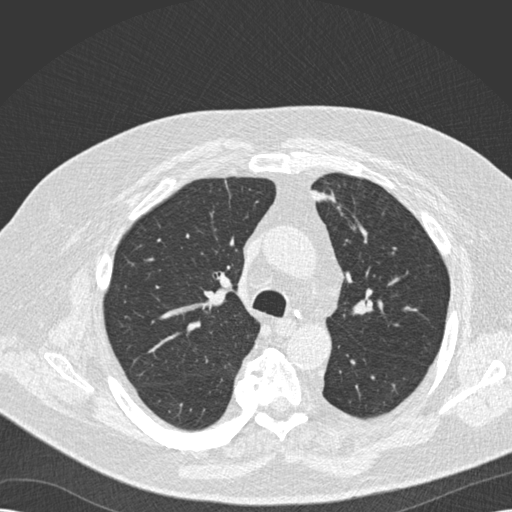
Low-dose screening chest CT, one axial slice. Slice 115 of 173 in the series (ordered by position). Reconstruction kernel B30f. 120 kVp. Lung window (W 1500 / L -600 HU). 512 × 512 image matrix, field of view 370 × 370 mm.
Annotated regions visible in this slice (manually delineated by an expert):
- lesion 1 (tumor, upper lobe of left lung): bounding box (x1, y1, x2, y2) in pixels: (312, 189, 327, 201)